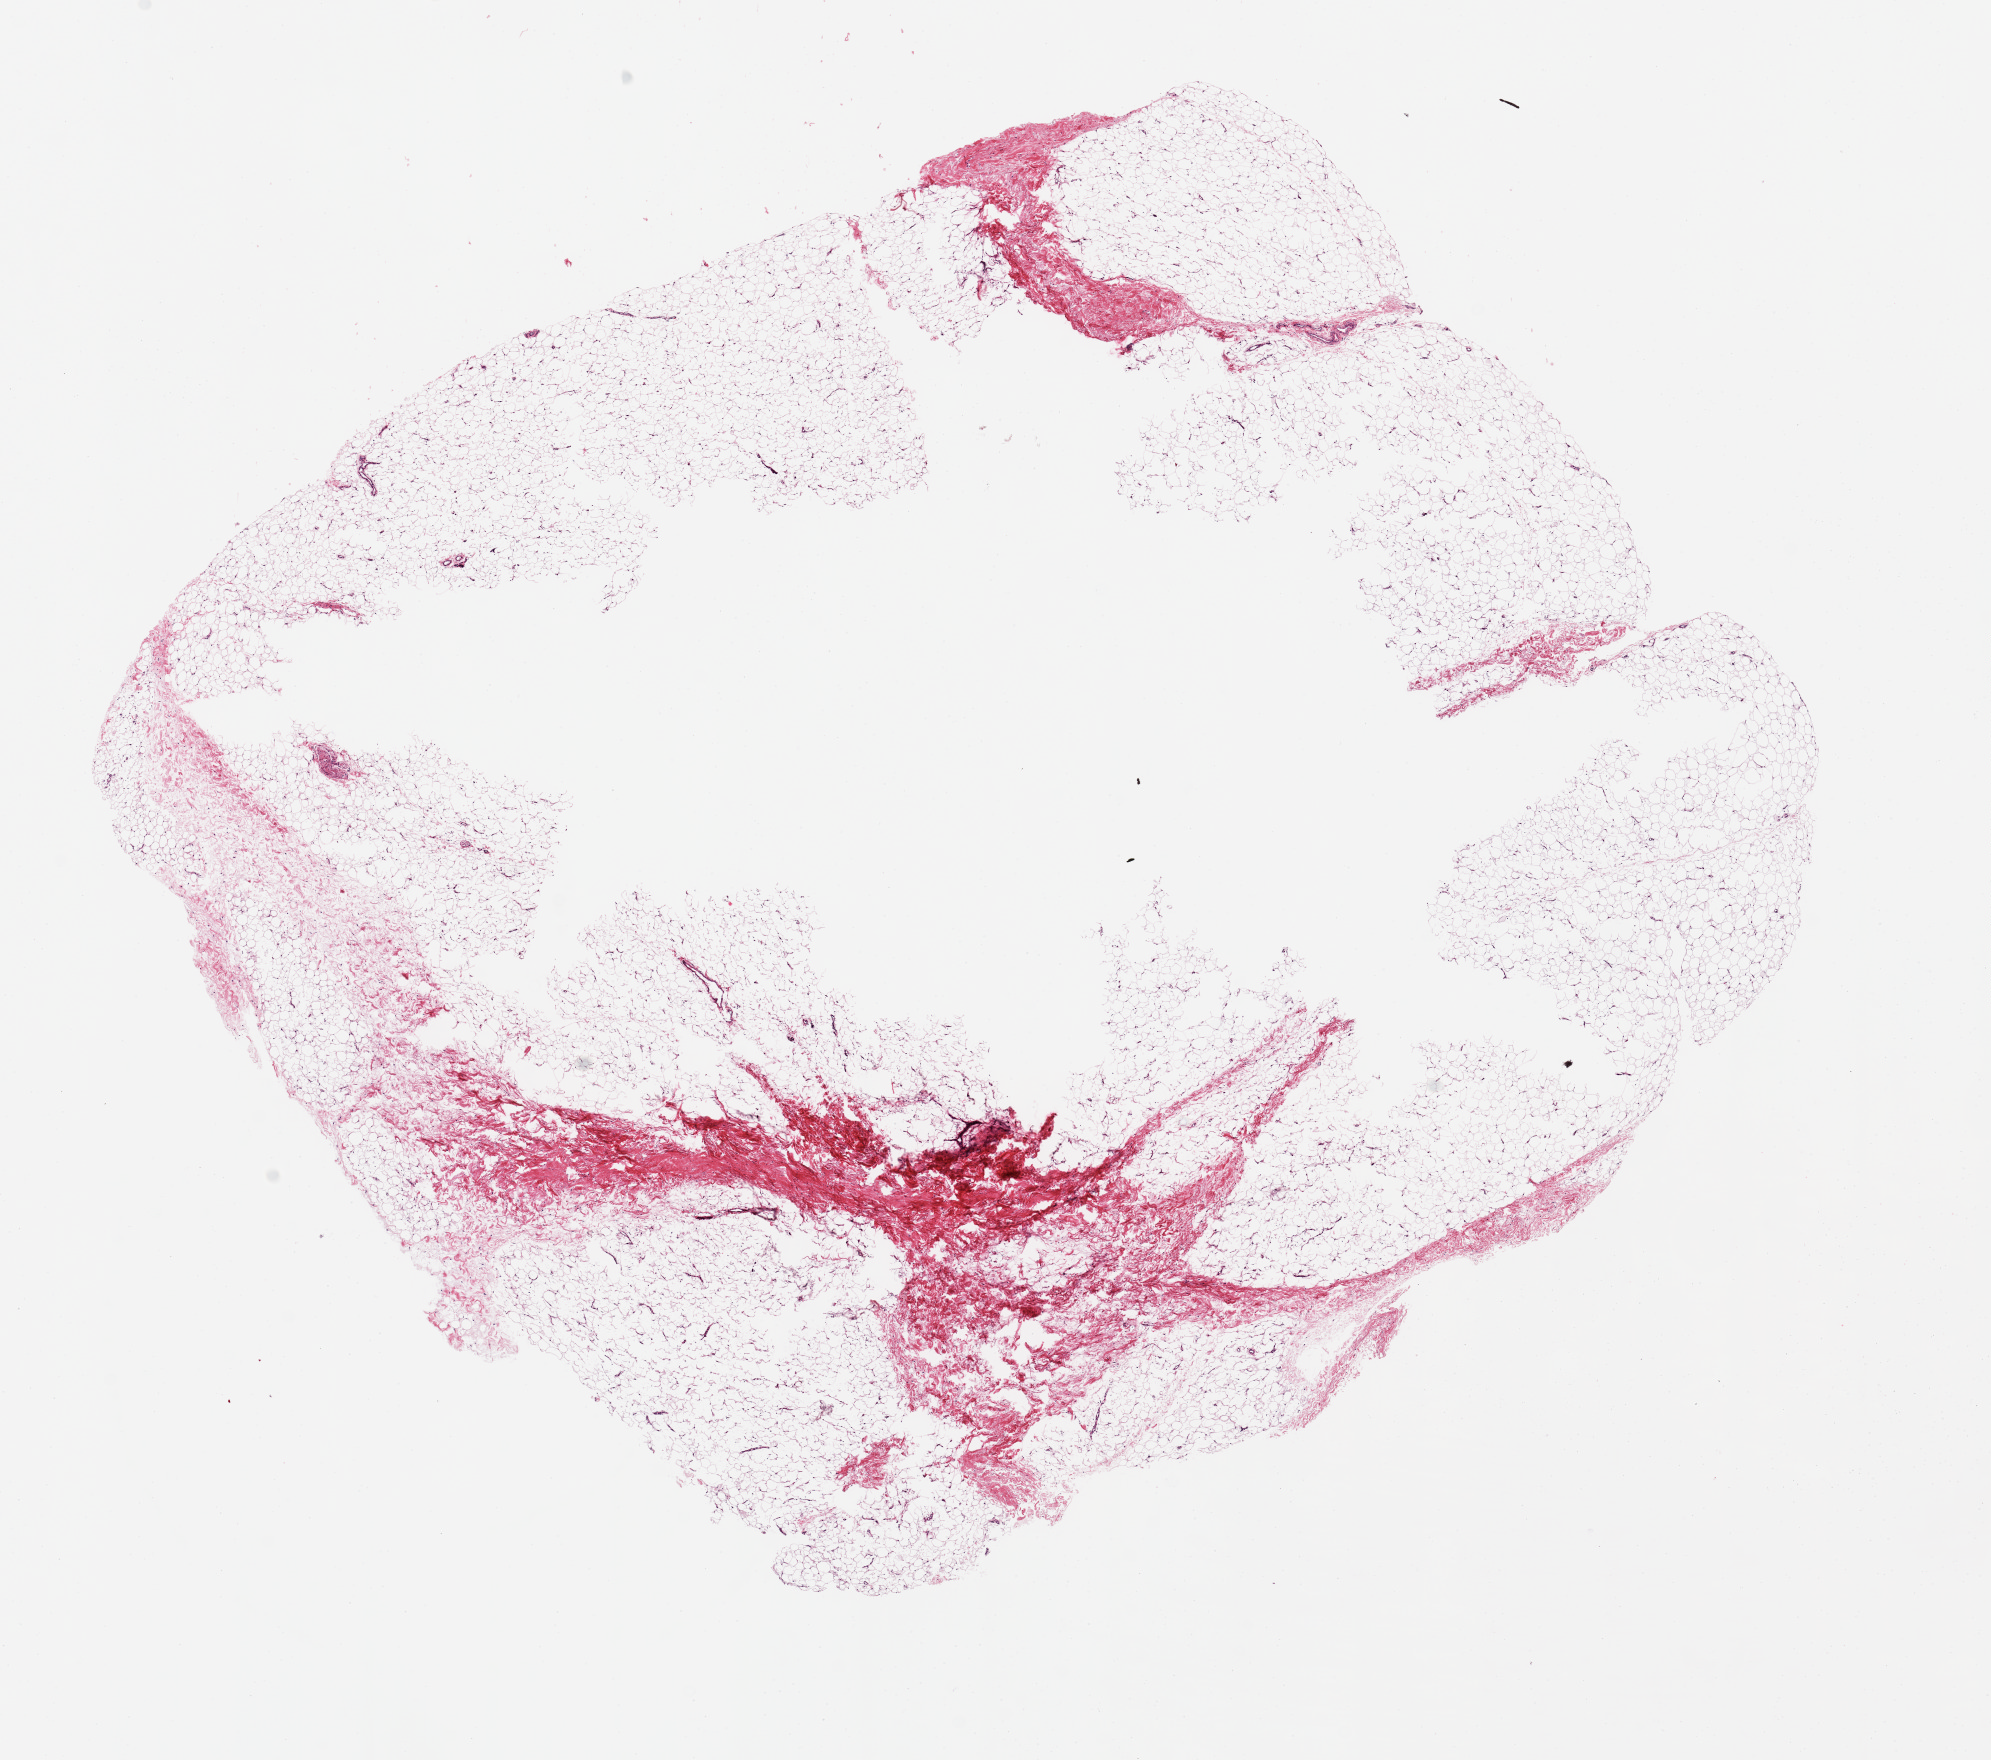
Whole-slide image, haematoxylin and eosin stain — low-resolution overview of the scanned area, about 15.8 x 13.9 mm (slide scanned at 20x), PAXgene-fixed, paraffin-embedded tissue, target tissue: adipose tissue, donor tissue sample. Donor: female.
Pathologist's review note for this sample: ~10x10mm. Central 60% unfixed with large hole/tear.